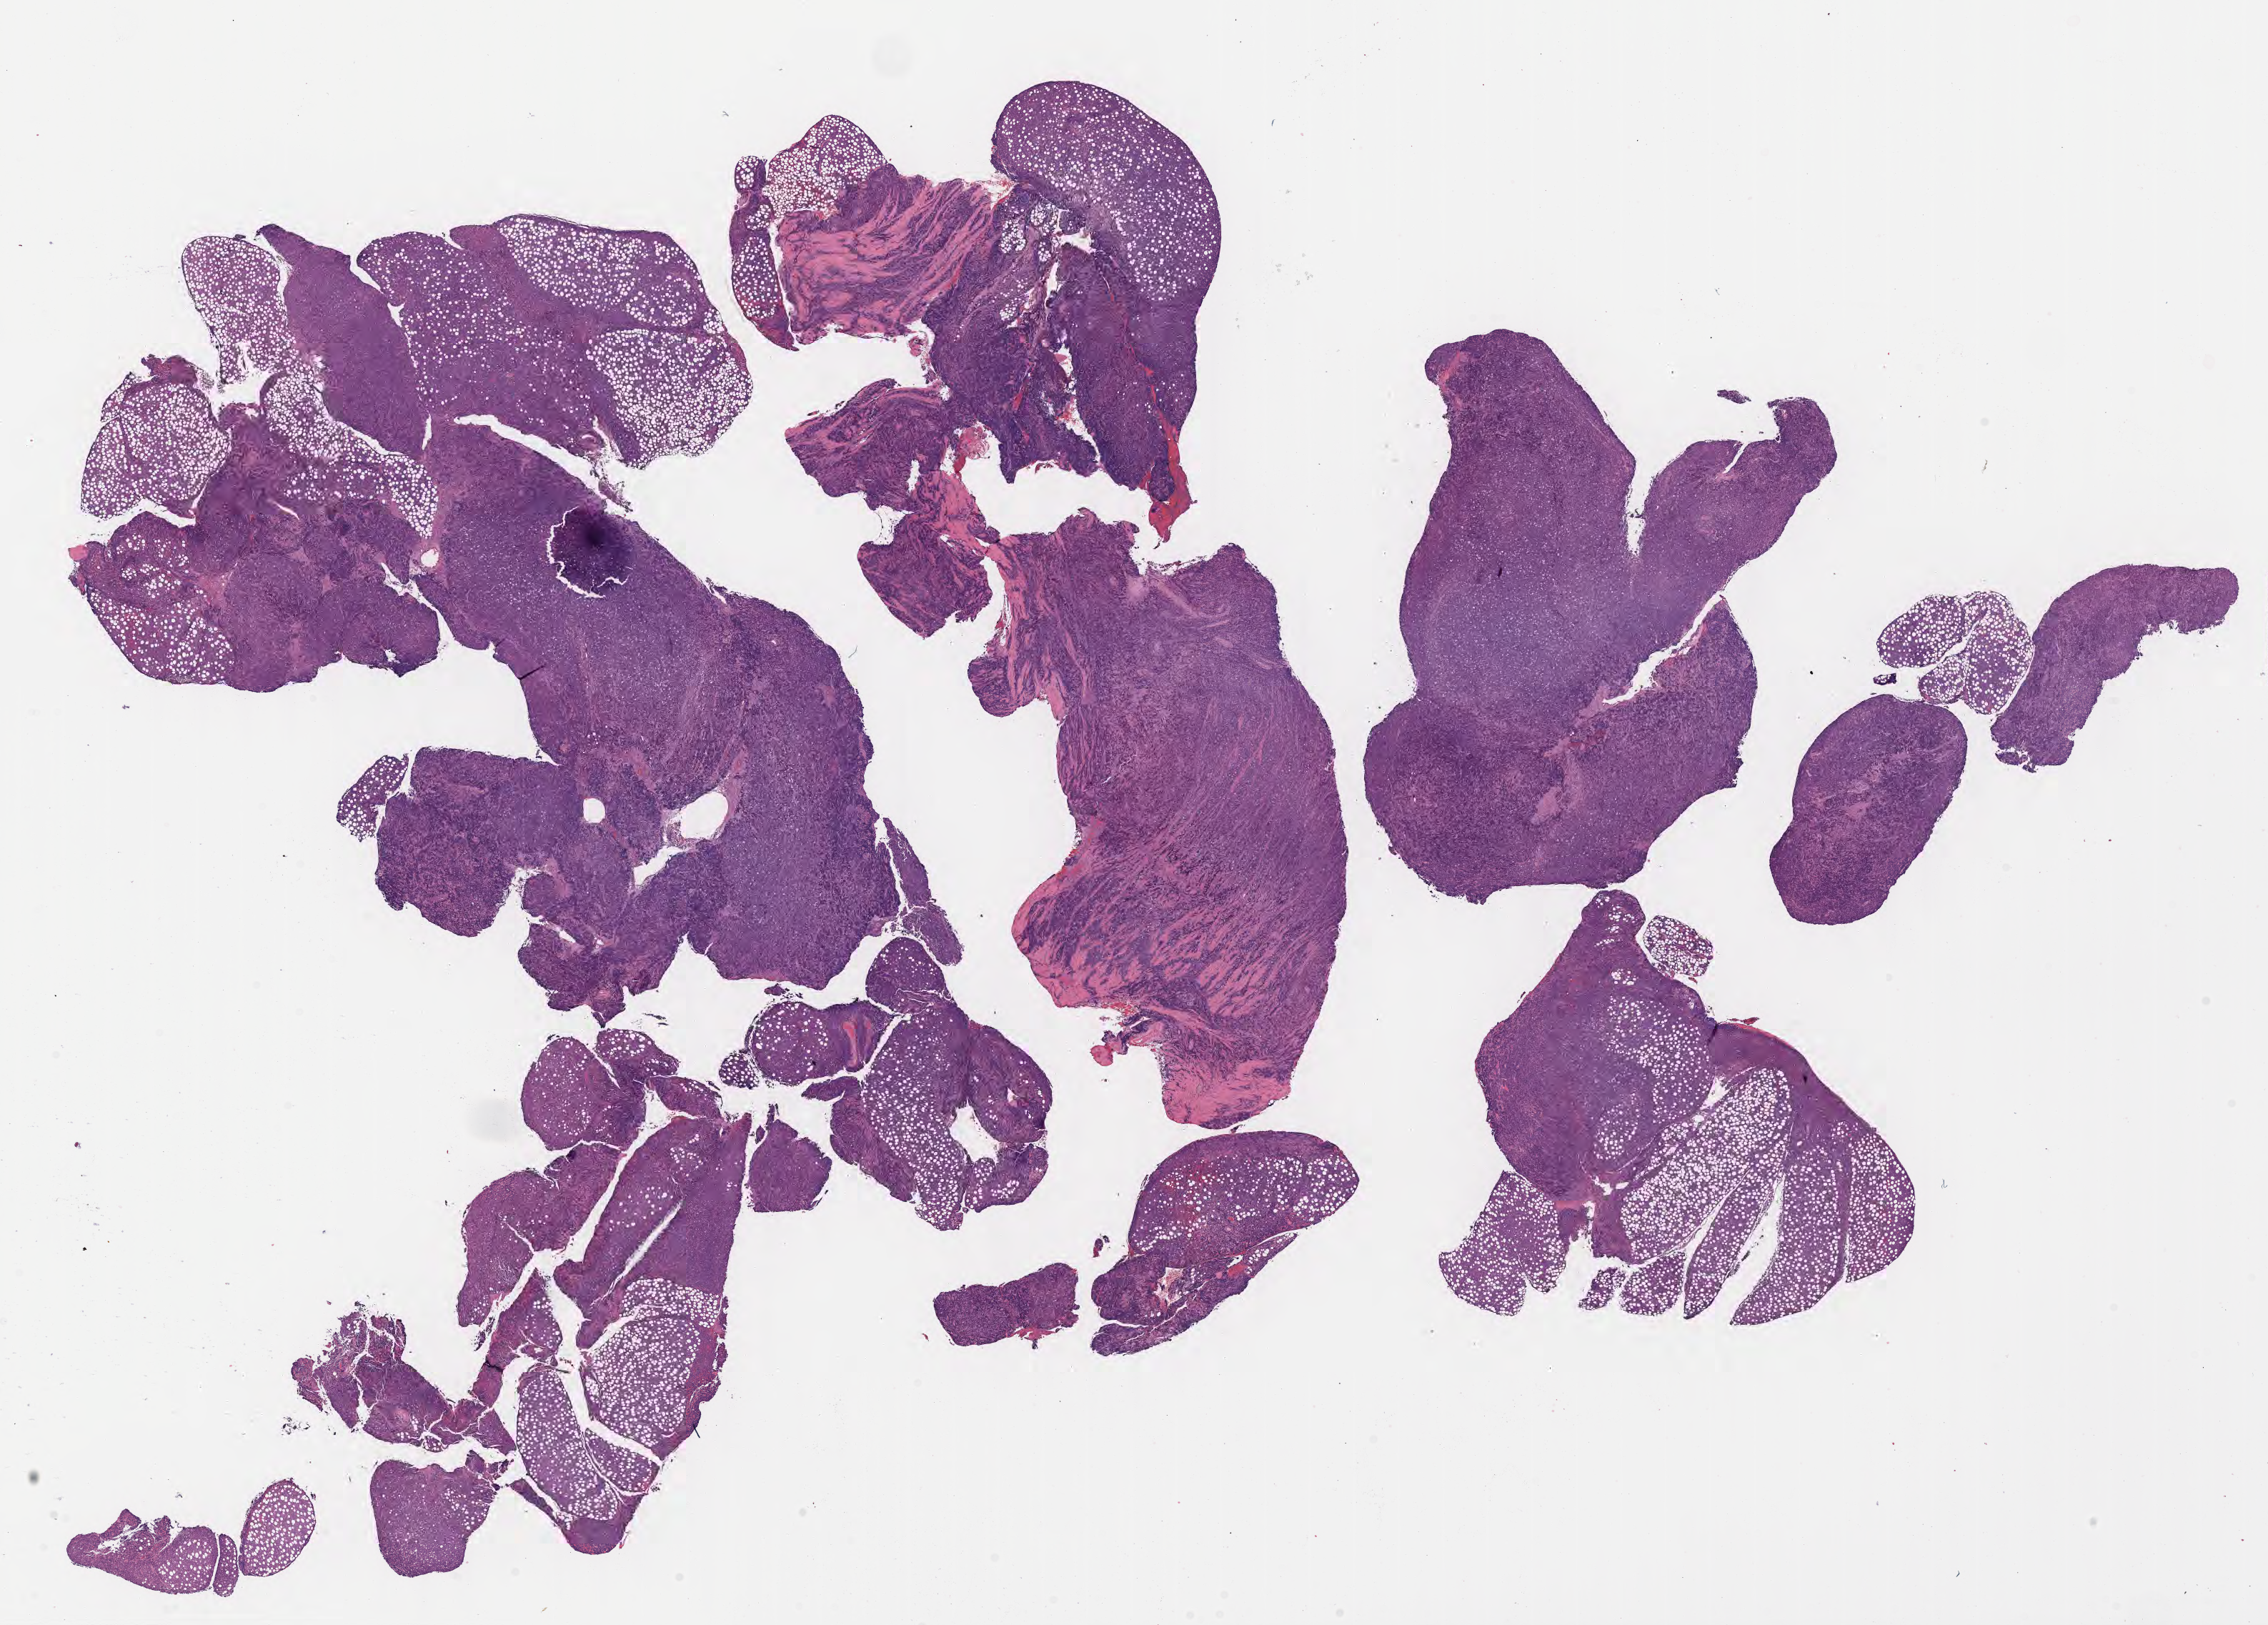
Whole-slide image, hematoxylin and eosin (H&E) stain — whole scanned area (about 25.7 x 18.4 mm) shown as a low-resolution overview; tumor tissue; site: abdomen proper. Patient: male, age at initial diagnosis 4 years.
Histologic diagnosis: Burkitt lymphoma, NOS.